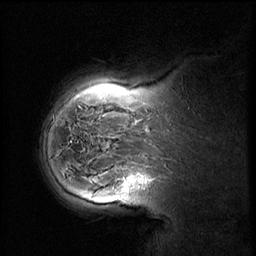
Breast MRI (dynamic contrast-enhanced), one sagittal slice. Position 45 of 58 along the scan axis. Dynamic contrast-enhanced series, image 2 of 2 at this slice position (ordered by acquisition). 1.5 T. TE 4.2 ms, TR 8.9 ms. 3 mm slice thickness. 256 × 256 image matrix. Patient: female, 37 years. From the clinical record (not read from this slice): setting: breast cancer imaged before/during neoadjuvant chemotherapy; receptor status: triple-negative.
Annotated regions visible in this slice (semi-automatically segmented with operator editing):
- analysis volume of interest (the breast-tissue region the enhancement analysis was run in; not a lesion): box from (x=114, y=160) to (x=166, y=207) px
- tumour enhancement mask (voxels above the 140 % enhancement threshold inside the analysis volume of interest): (x=125, y=174)–(x=148, y=187)